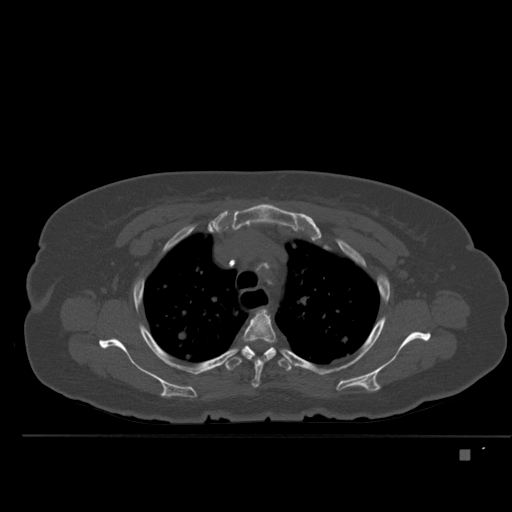
CT including the spine, one axial slice. Position 375 of 477 along the scan axis. Bone window (W 1800 / L 400 HU). 512 × 512 image matrix. Patient: female, 74 years. From the clinical record (not read from this slice): primary cancer: colon.
Annotated regions visible in this slice (semi-automatically segmented with operator editing):
- T3 vertebra: bounding box <241,309,277,388> (left, top, right, bottom; pixels)
- T4 vertebra: <224,345,292,371>